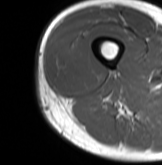
MRI of an extremity soft-tissue mass, one axial slice. Slice 21 of 61 in the series (ordered by position). MR volume resampled by the dataset authors to the PET/CT grid (not the native acquisition matrix). 3.27 mm slice thickness. 162 × 165 image matrix, field of view 158 × 161 mm. Male patient. Case-level facts recorded for this patient, not image findings: histological type: poorly differentiated synovial sarcoma; grade: high; site of the primary tumour: right buttock.
Annotated regions visible in this slice (expert contour drawn on MRI and transferred to this co-registered scan by the dataset authors):
- gross tumour volume including surrounding oedema: bounding box (x1, y1, x2, y2) in pixels: (52, 42, 99, 92)